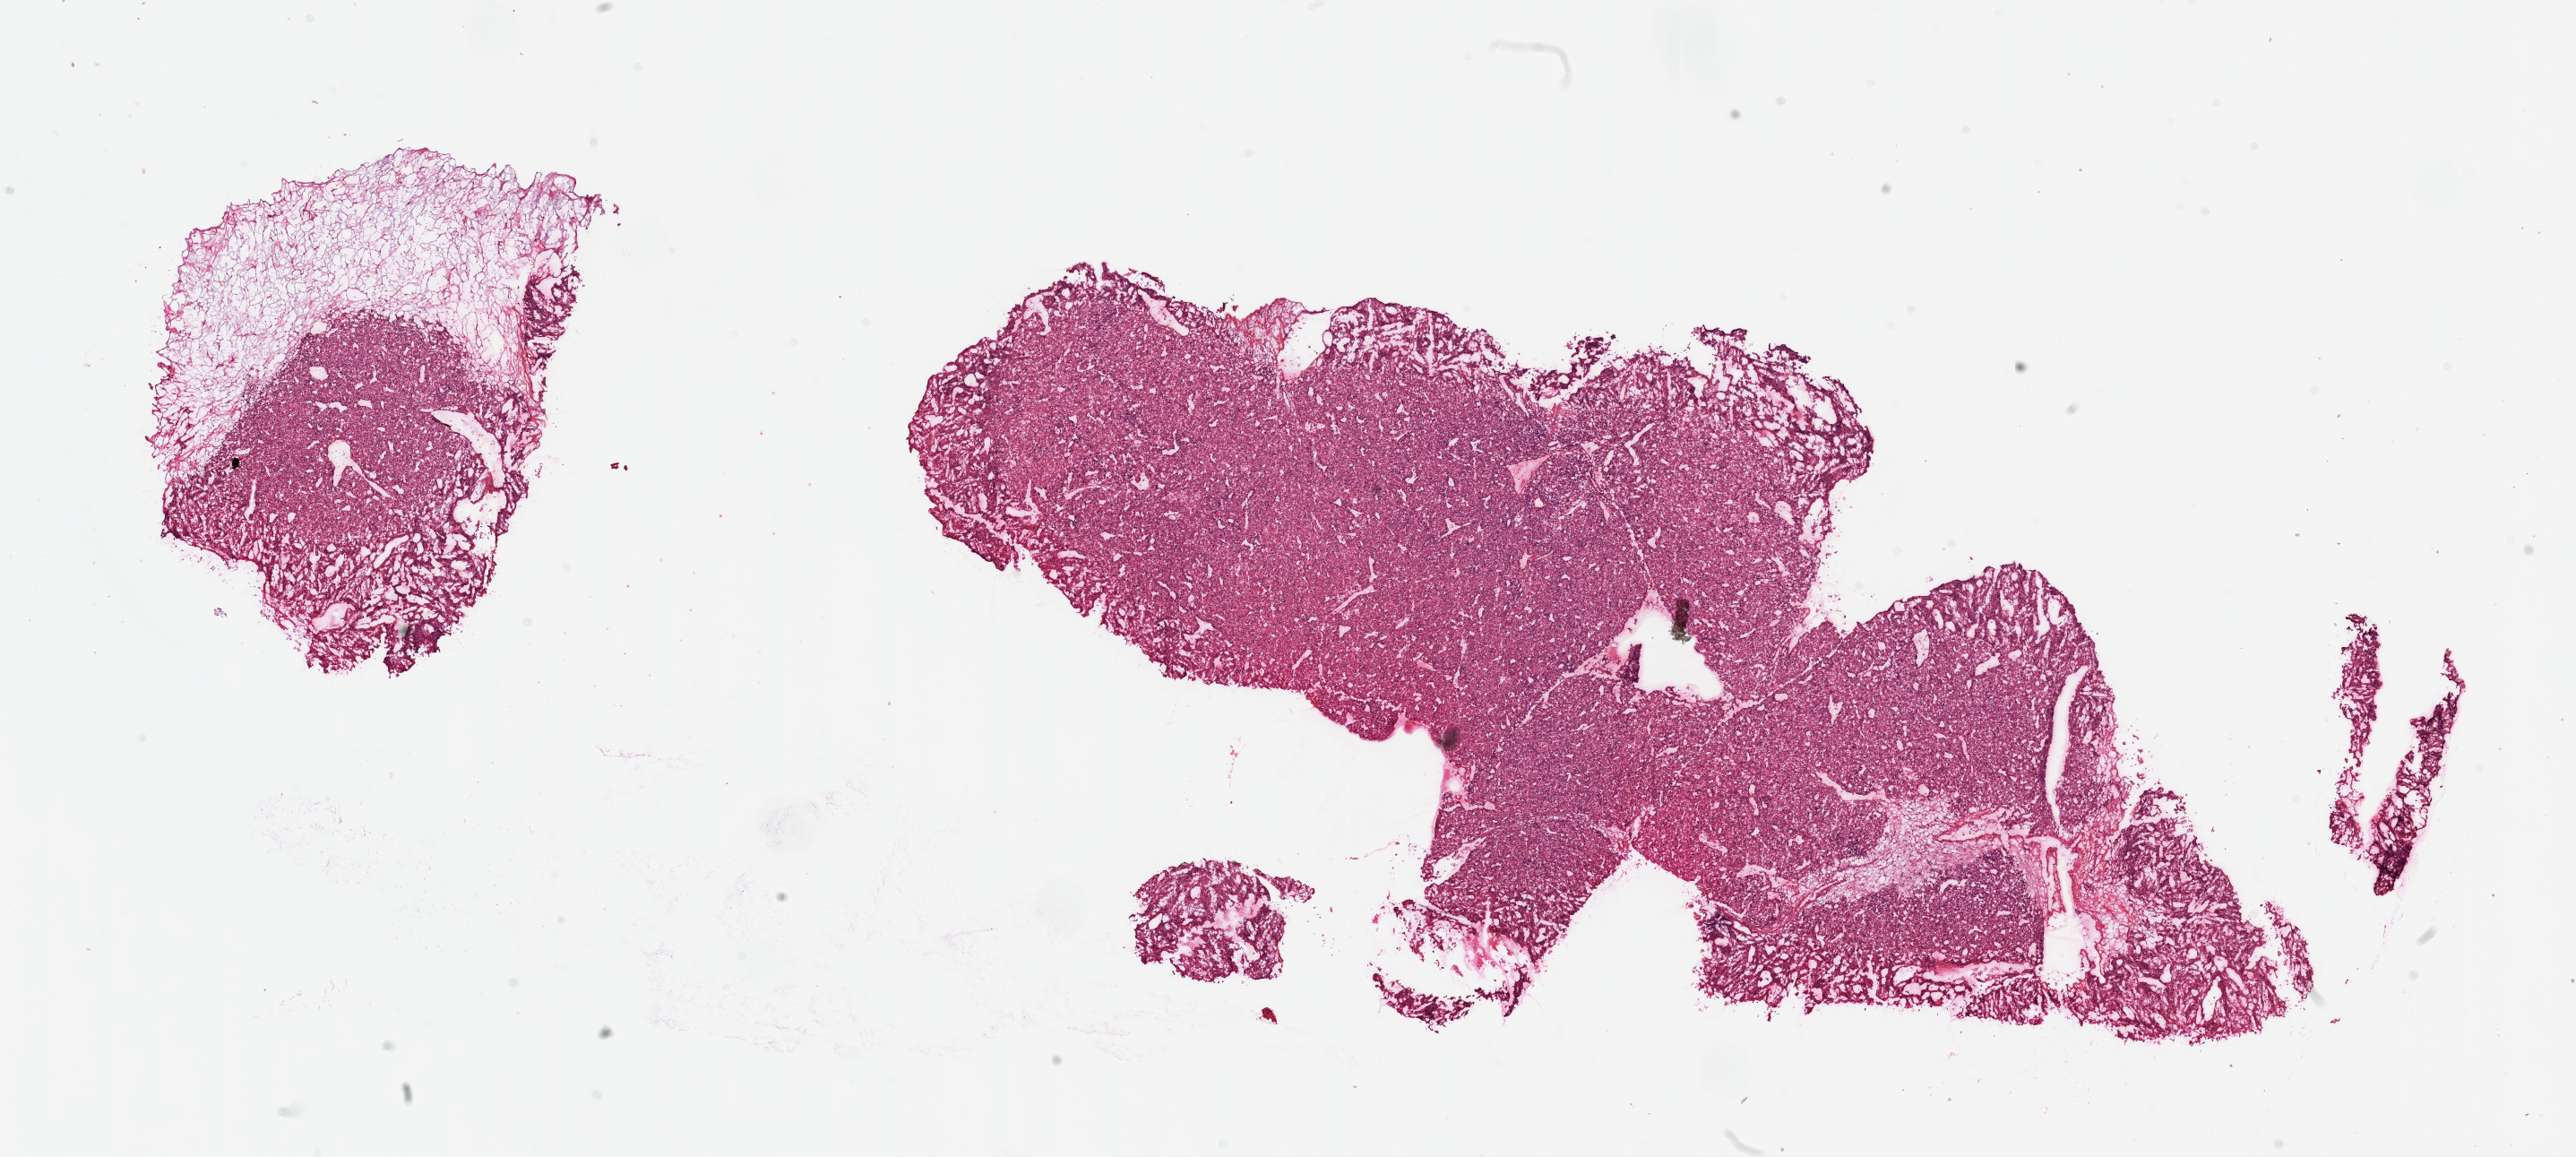
H&E whole-slide image — whole scanned area (about 23.1 x 10.4 mm) shown as a low-resolution overview; frozen section from the top of the tissue portion; sample: primary tumour, kidney. Patient: male, age at initial diagnosis 48 years.
Histologic diagnosis: Clear cell adenocarcinoma, NOS.